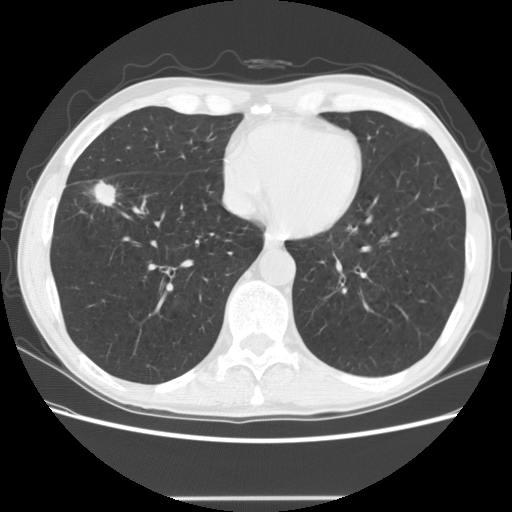
Low-dose screening chest CT, axial slice; first (baseline) screen; lung window (W 1500 / L -600 HU); standard (soft-tissue) reconstruction kernel (STANDARD); 512 × 512 image matrix. Male participant, aged 69 years at enrolment.
• Expert reader's lesion annotation, bounding box (x1, y1, x2, y2) in pixels: (73, 165, 130, 216).
• The exam's reader record, not a measurement of the box and not confirmed to be the same lesion: non-calcified nodule or mass ≥4 mm, right middle lobe, 20 × 14 mm, spiculated (stellate) margins, mixed attenuation.
• Official screen result: positive, change unspecified: nodule(s) >= 4 mm or enlarging nodule(s), mass(es), or other non-specific abnormalities suspicious for lung cancer.